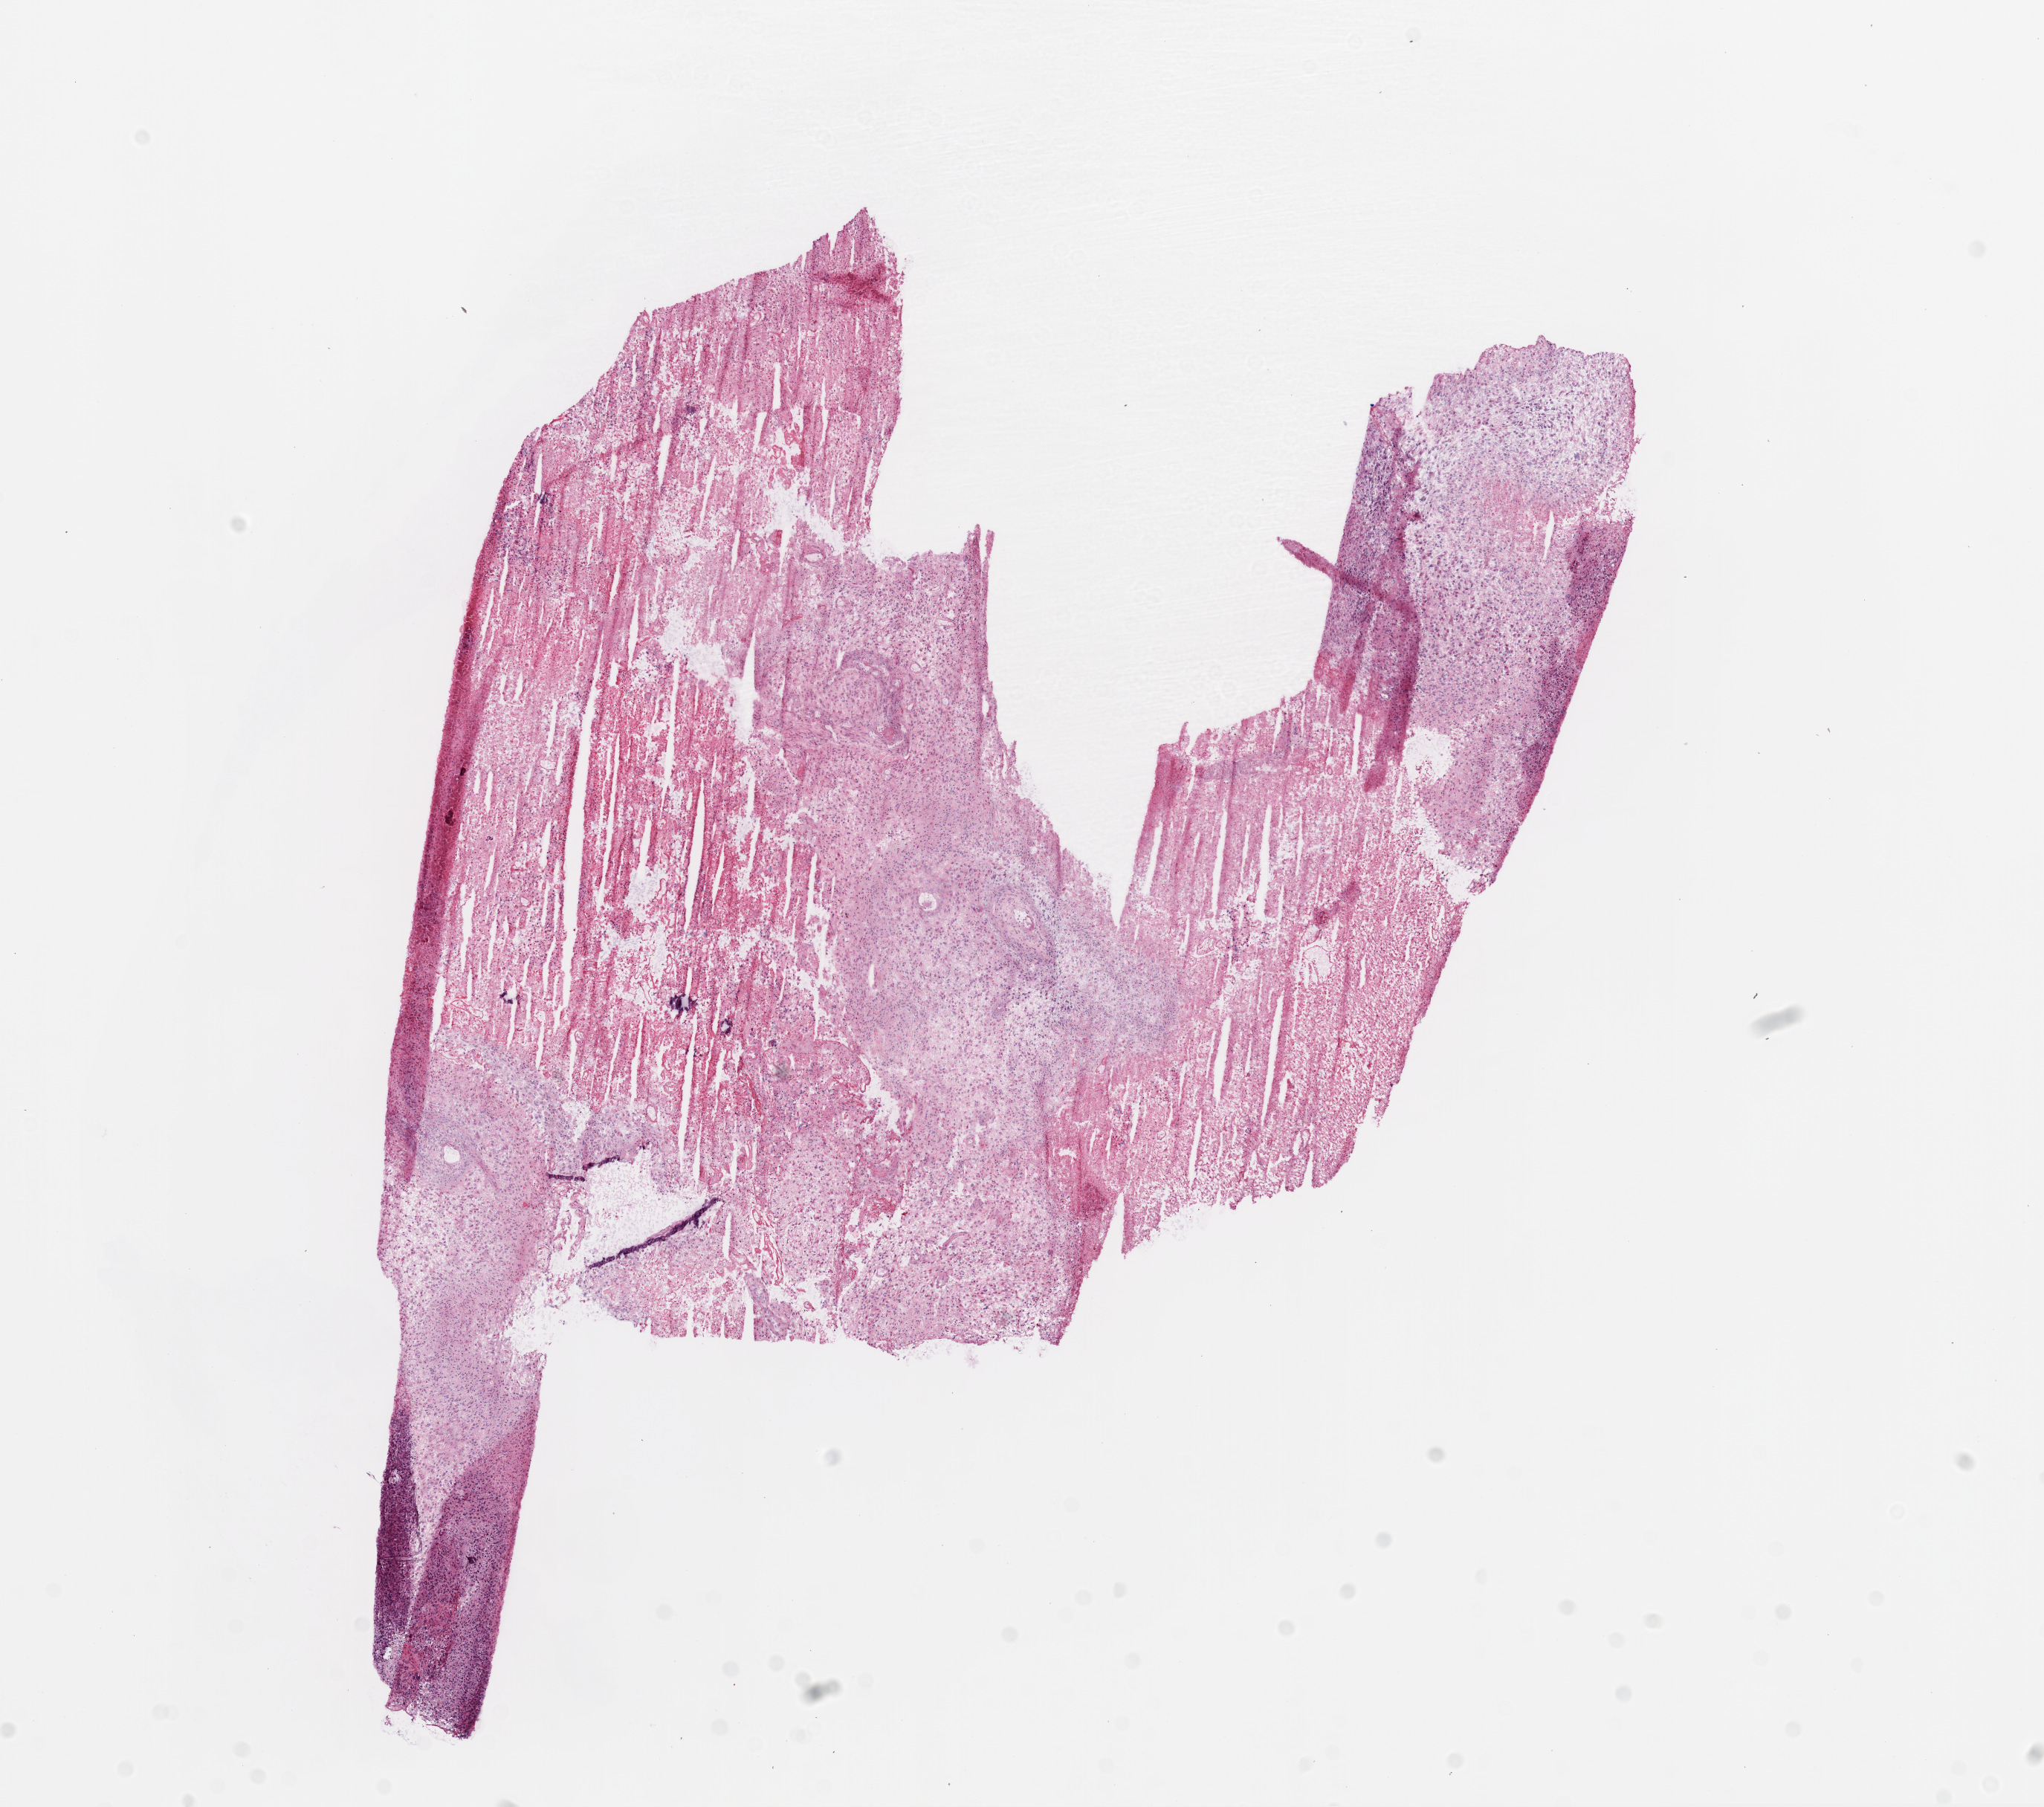
Whole-slide histology image, H&E-stained — low-resolution overview of the scanned area, about 11.0 x 9.8 mm (slide scanned at 20x). Frozen section from the top of the tissue portion. Sample: primary tumour, brain. Male patient; age at initial diagnosis 62 years. Composition of this section per pathologist review: tumour cells 70%, tumour nuclei 85%, normal cells 0%, stromal cells 0%, necrosis 30%.
Diagnosis: Glioblastoma.